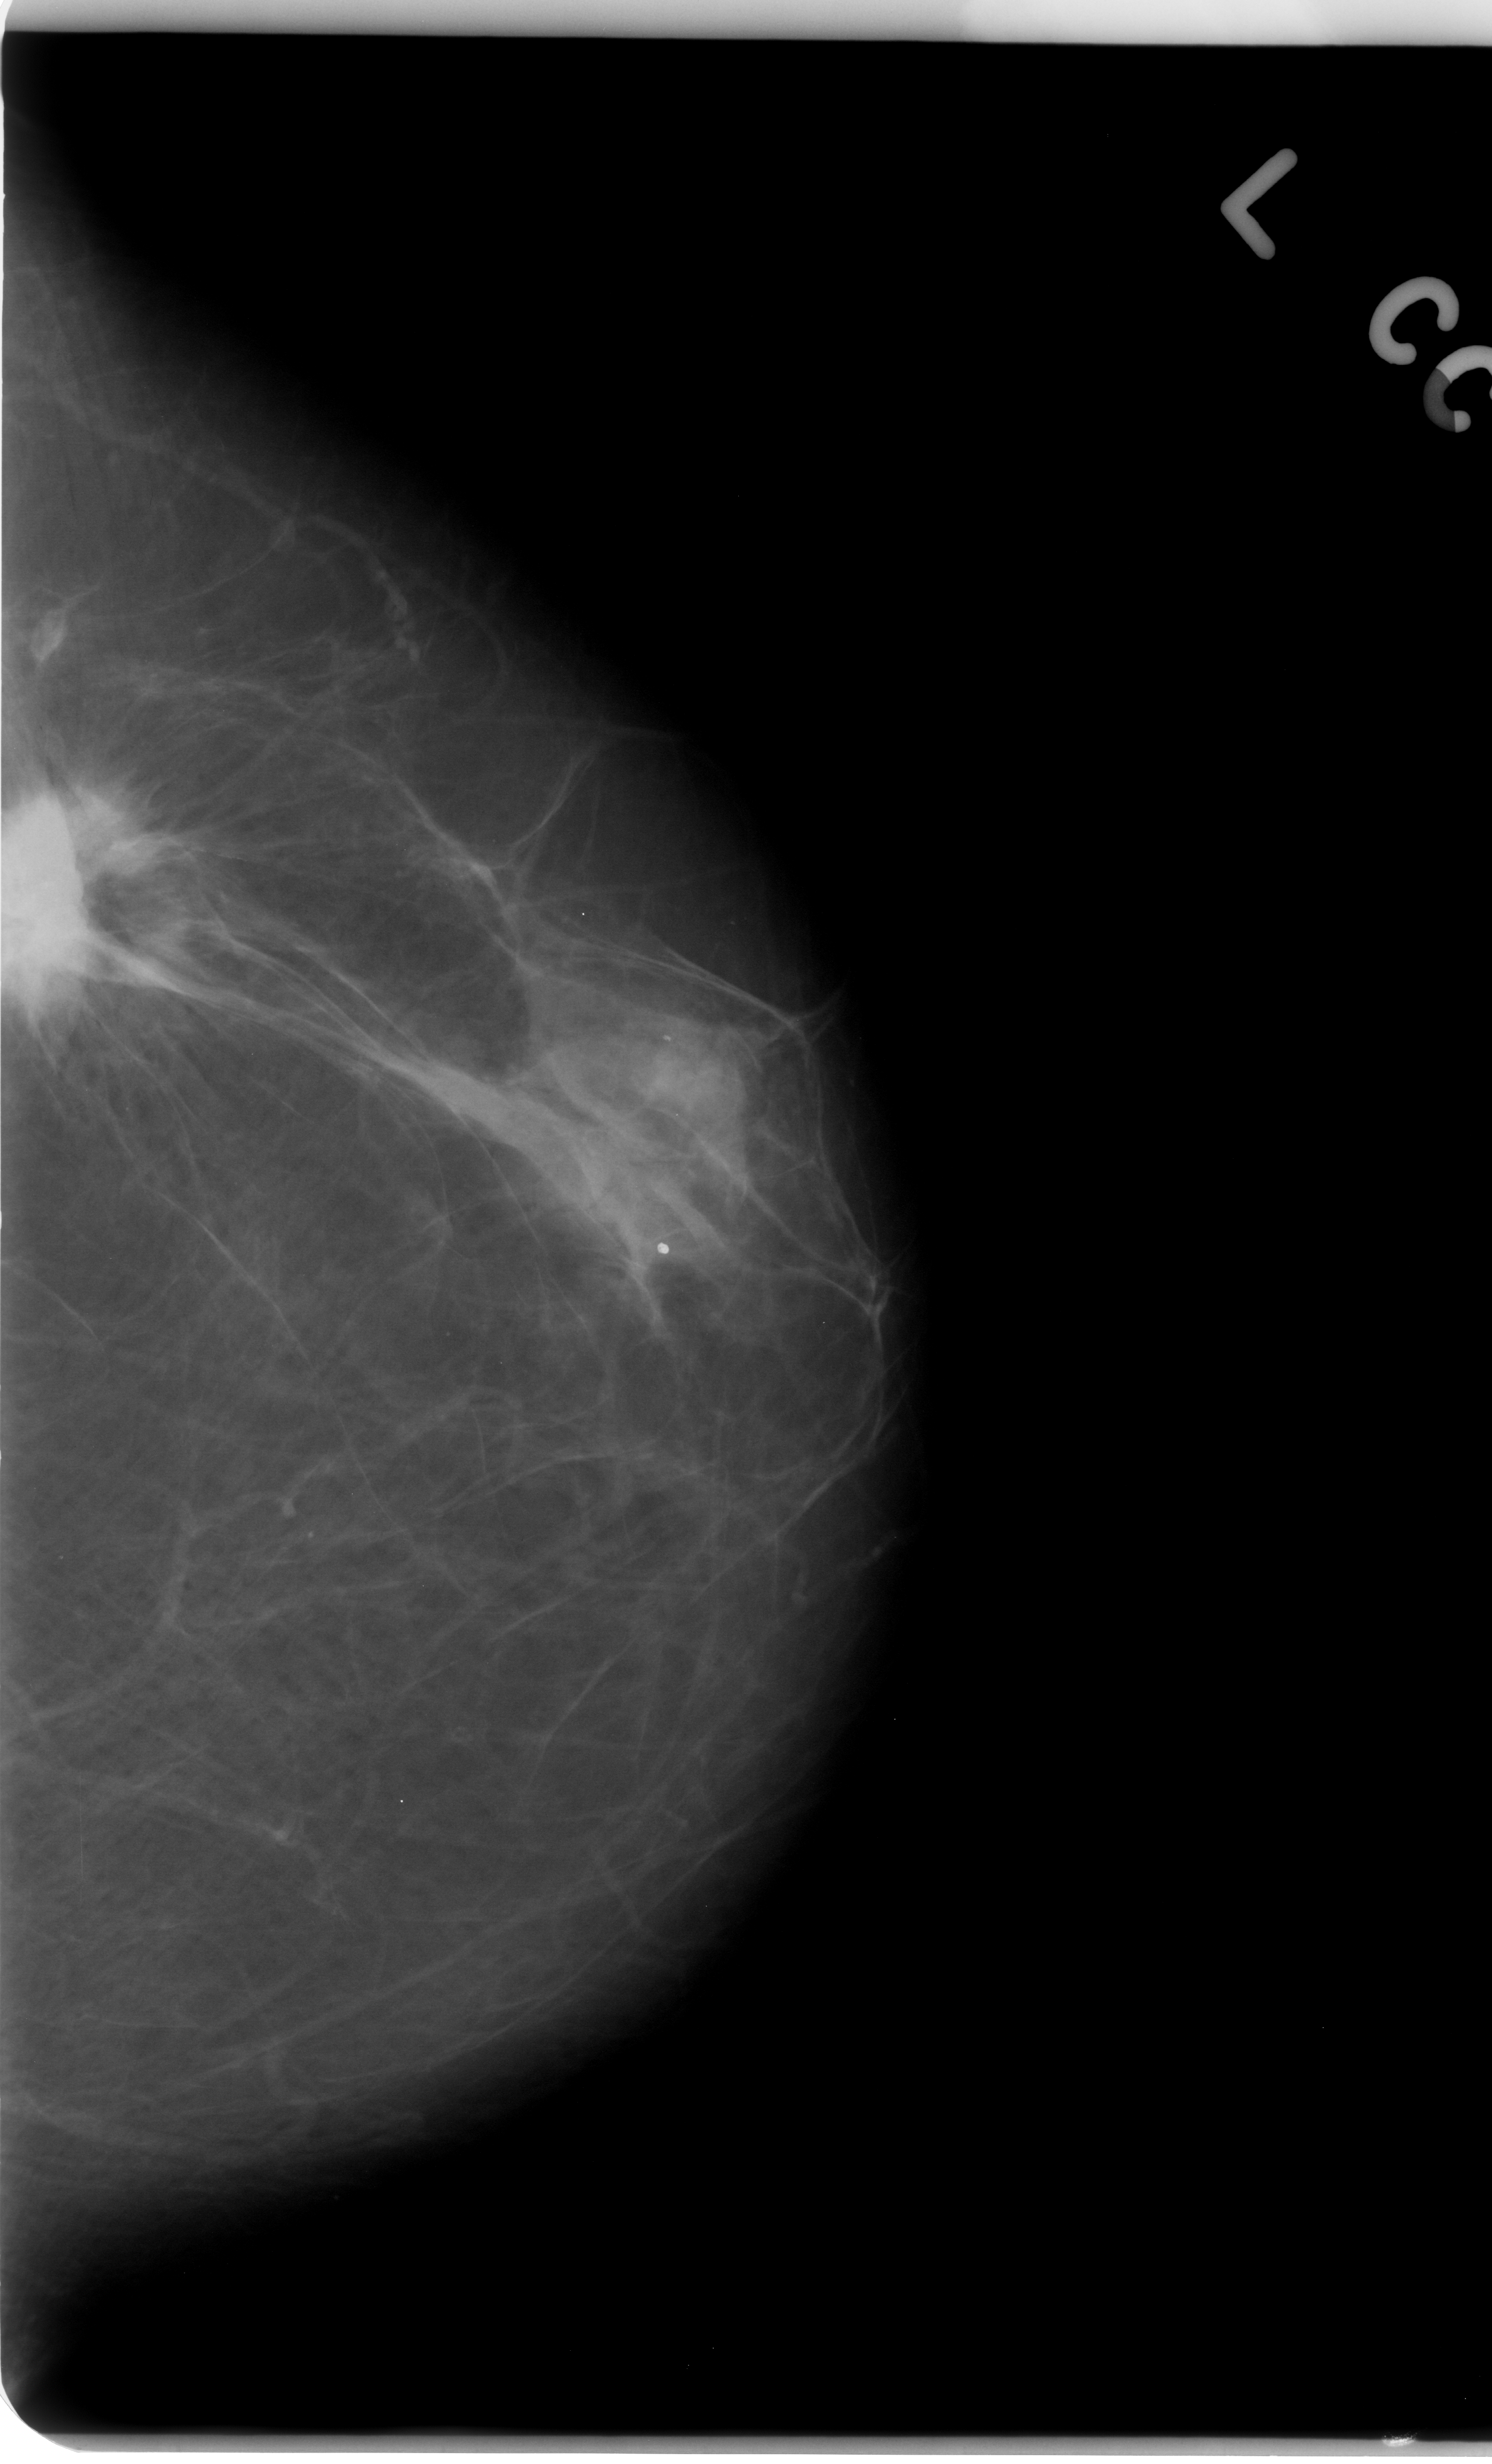
Scanned film-screen mammogram; left breast; craniocaudal (CC) view; BI-RADS breast density category 1 (scale 1–4).
Abnormality record for this image: mass, shape irregular, margins spiculated; BI-RADS assessment category 5; pathology (as recorded): malignant.